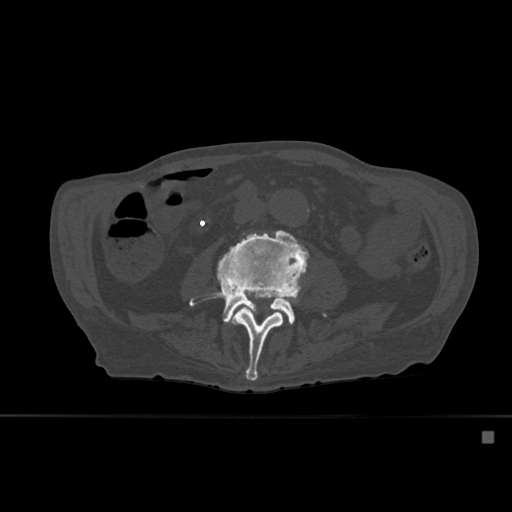
CT including the spine, one axial slice; position 205 of 527 along the scan axis; bone window (W 1800 / L 400 HU); 512 × 512 image matrix. Patient: male, 78 years. From the clinical record (not read from this slice): primary cancer: prostate.
Annotated regions visible in this slice (semi-automatically segmented with operator editing):
- L3 vertebra: box from (x=228, y=277) to (x=298, y=381) px
- L4 vertebra: (x=190, y=230)–(x=326, y=325)